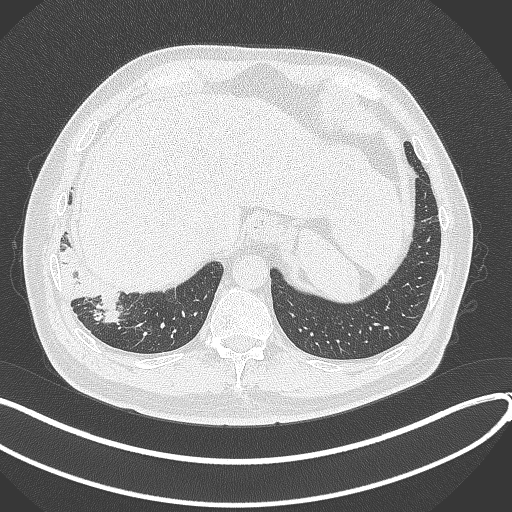
Chest CT, one axial slice; position 55 of 360 along the scan axis; reconstruction kernel B70f; 120 kVp; lung window (W 1500 / L -600 HU); 512 × 512 image matrix. Patient: male, 59 years.
Outlined on this slice (rectangle marked by the reading radiologist):
- lung tumour (recorded histology: adenocarcinoma): box from (x=62, y=244) to (x=122, y=327) px